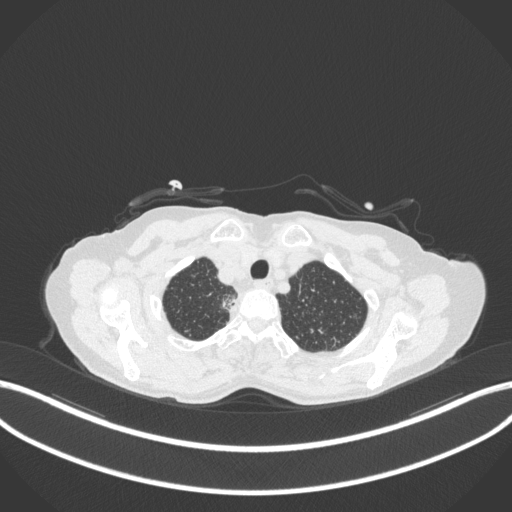
Chest CT, one axial slice; slice 333 of 363 in the series (ordered by position); reconstruction kernel B31f; lung window (W 1500 / L -600 HU); 1 mm slice thickness; 512 × 512 image matrix. Female patient, age 75 years. From the clinical record (not read from this slice): clinical TNM (as recorded): T1c N1 M1.
Annotated regions visible in this slice (bounding box drawn by a radiologist):
- lung tumour (recorded histology: adenocarcinoma): box from (x=219, y=293) to (x=240, y=311) px